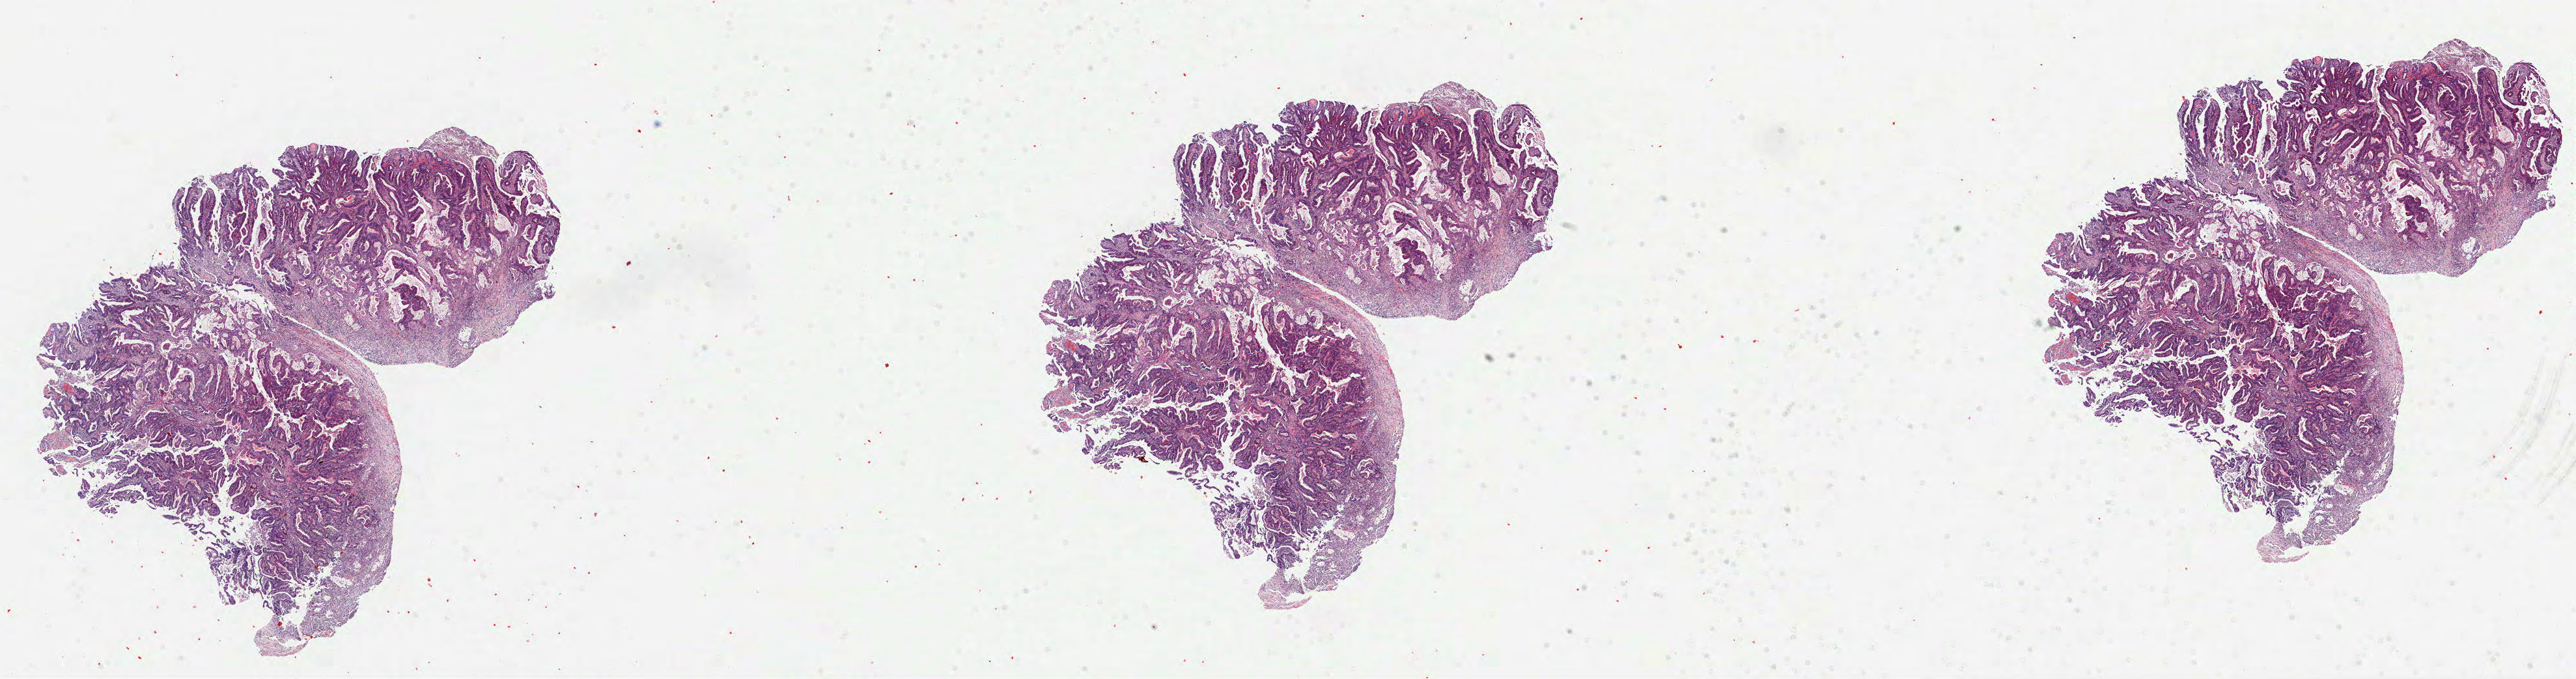
Whole-slide histology image, H&E-stained — shown as a low-resolution overview of the whole scanned area (about 31.9 x 8.4 mm, acquisition: 40x scan). FFPE section. Primary tumour sample from the colon. Patient: female, age at initial diagnosis 69 years.
Lymph nodes positive (case pathology): 0 of 16 examined. TNM: T2 N0 M0. AJCC pathologic stage: I (7th edition). Histologic diagnosis: Adenocarcinoma, NOS.